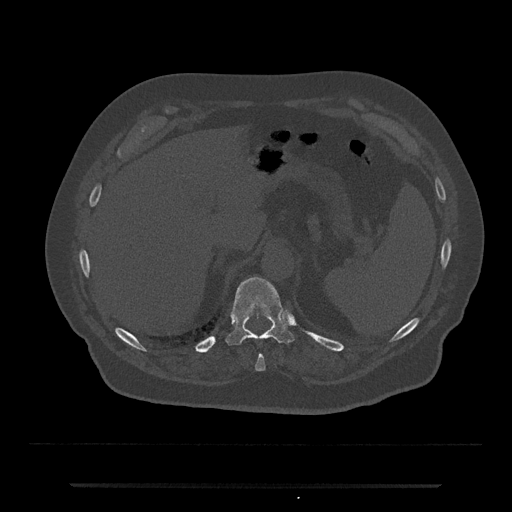
CT including the spine, one axial slice; slice 659 of 797 in the series (ordered by position); 120 kVp; bone window (W 1800 / L 400 HU); 0.5 mm slice thickness; 512 × 512 image matrix, field of view 434 × 434 mm. Male patient, age 80 years. Case-level facts recorded for this patient, not image findings: primary cancer: prostate.
Structures marked on this image (semi-automatic segmentation, software-assisted and operator-edited):
- T10 vertebra: bounding box <255,354,266,371> (left, top, right, bottom; pixels)
- T11 vertebra: <225,277,294,346>